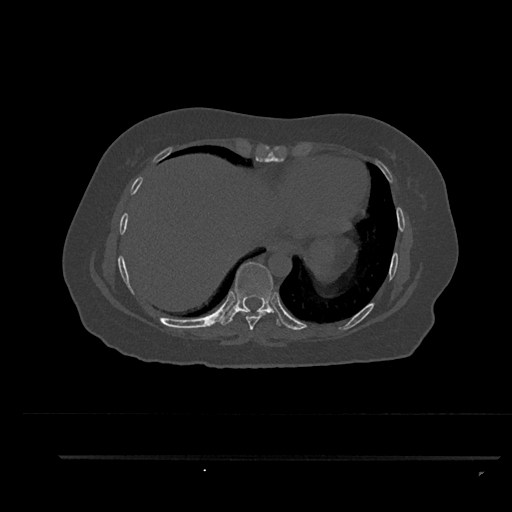
CT including the spine, one axial slice. Slice 434 of 797 in the series (ordered by position). Bone window (W 1800 / L 400 HU). 512 × 512 image matrix, field of view 408 × 408 mm. Female patient, age 44 years. From the clinical record (not read from this slice): primary cancer: renal.
Outlined on this slice (semi-automatic segmentation, software-assisted and operator-edited):
- T8 vertebra: box from (x=238, y=310) to (x=267, y=330) px
- T9 vertebra: (x=220, y=262)–(x=284, y=326)